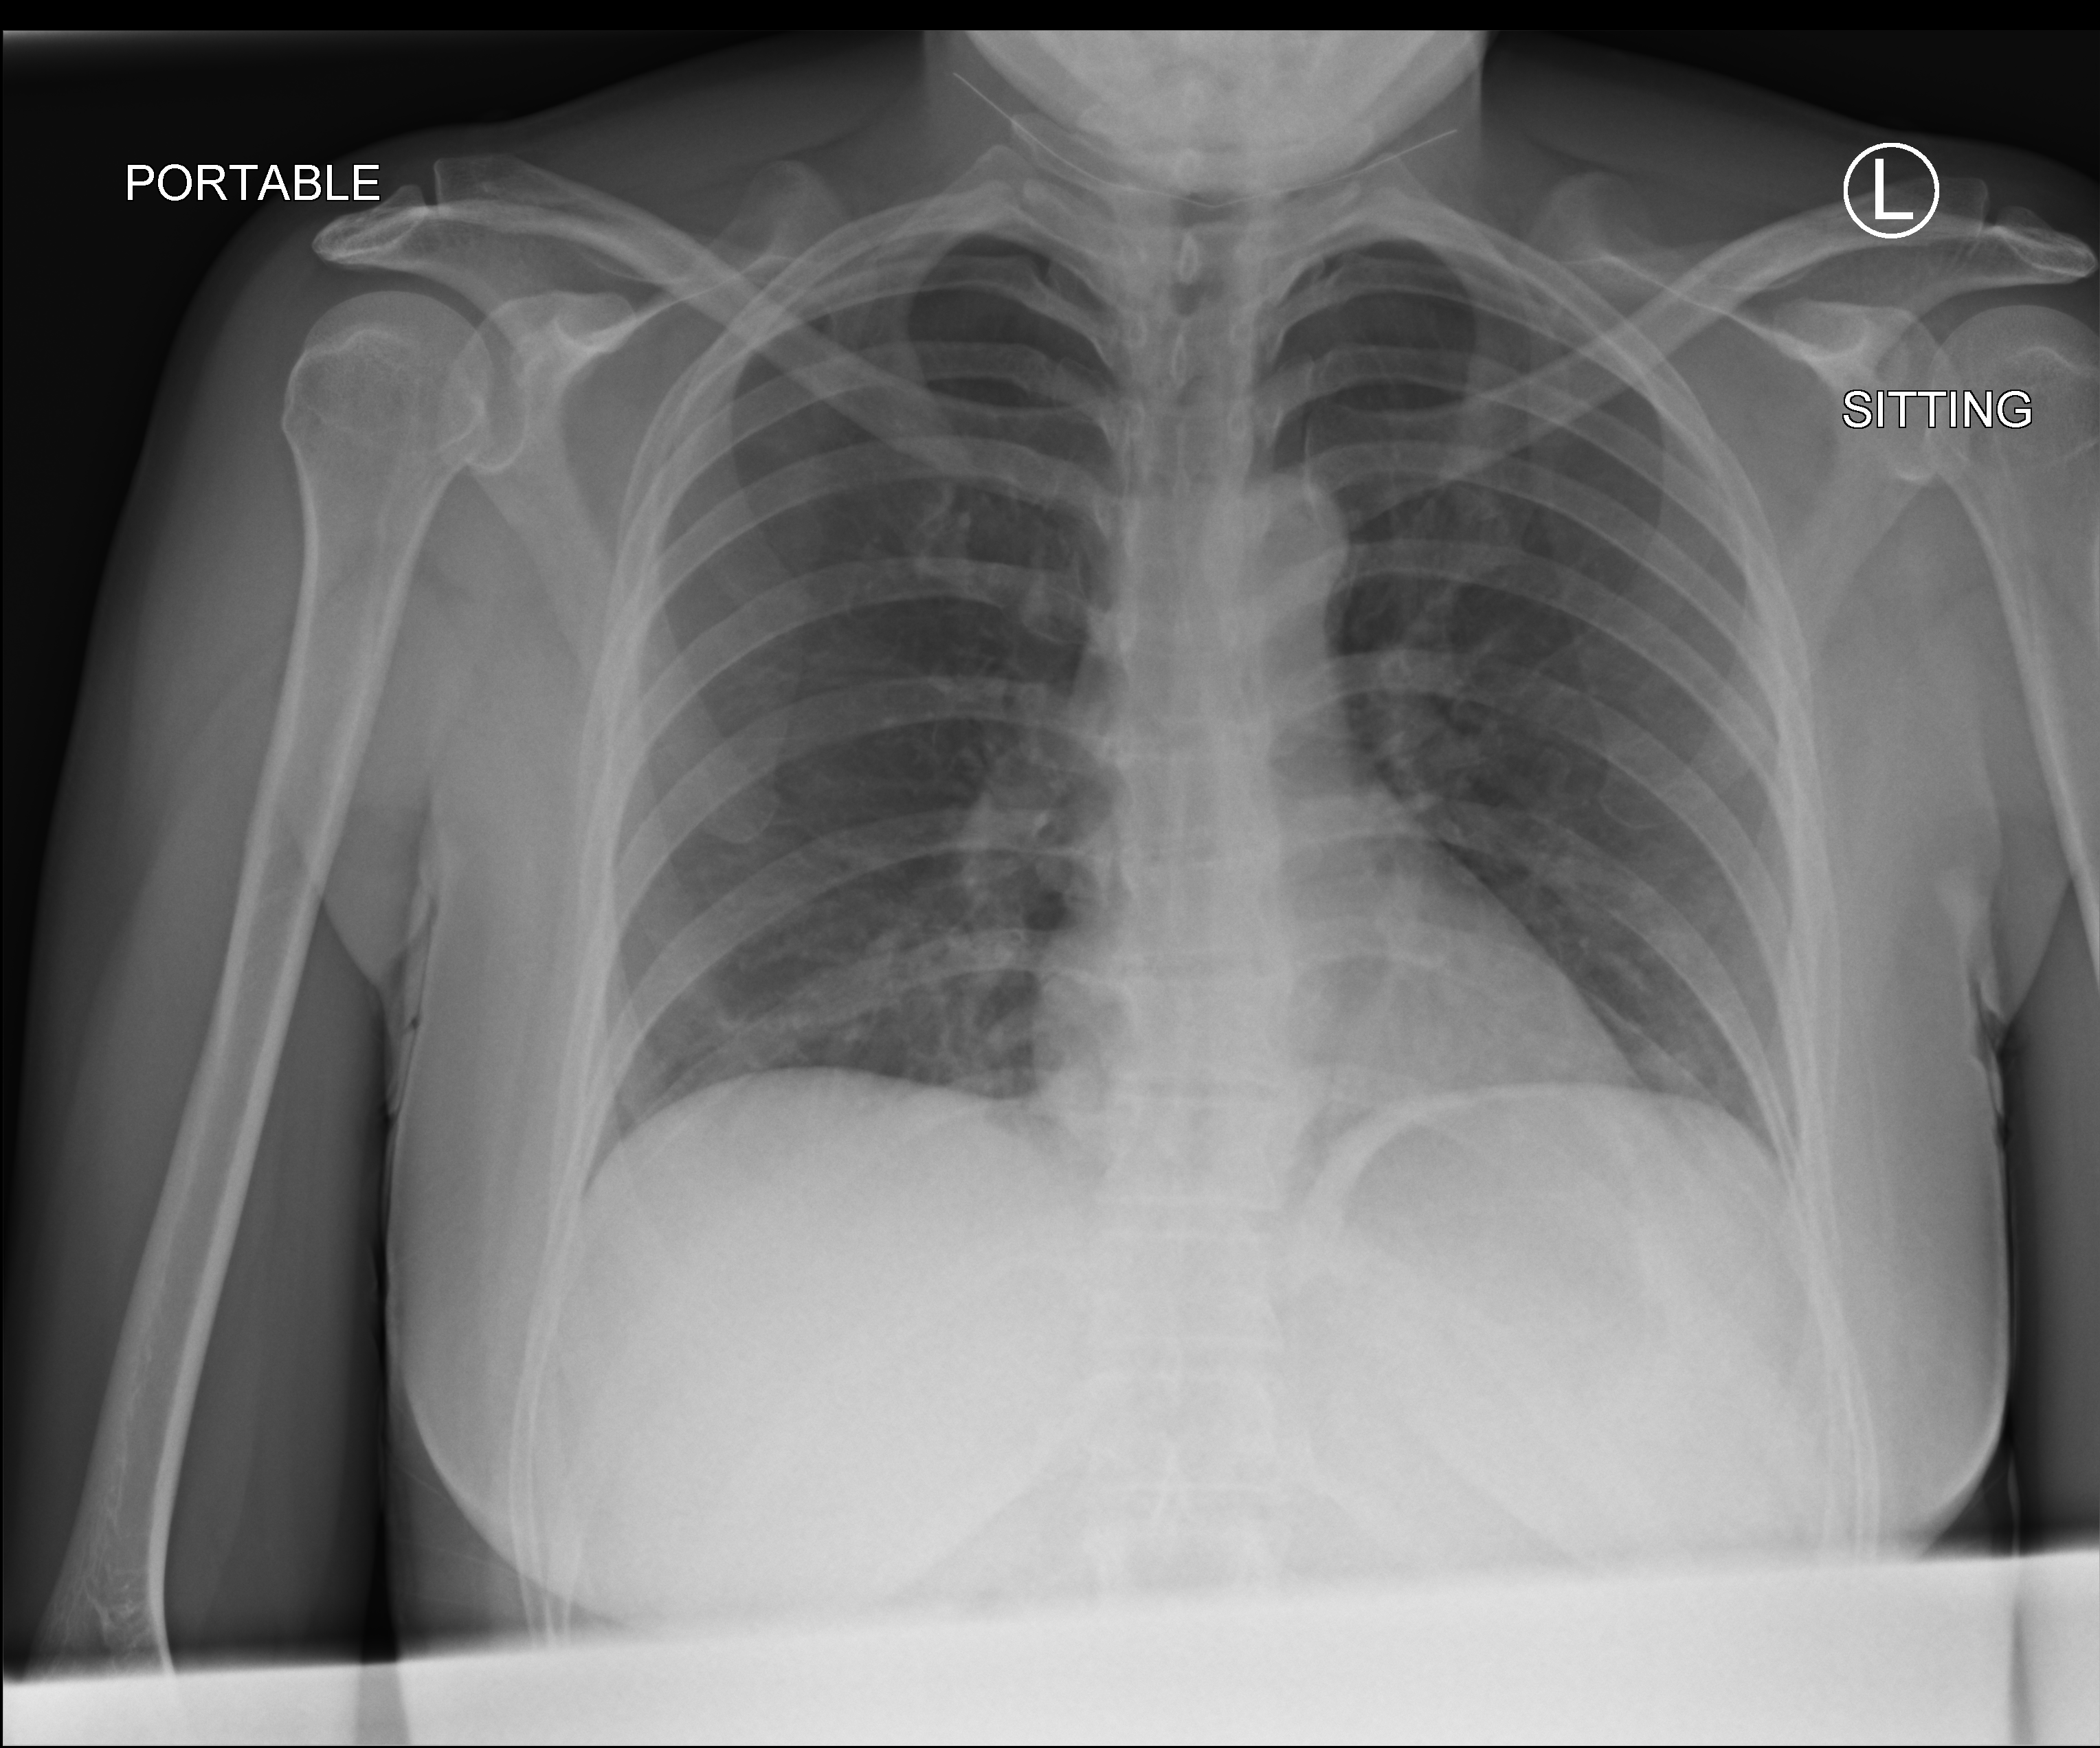
Chest X-ray (portable). Female patient hospitalised with COVID-19, age 18–59 years.
From the hospital-stay record, not from the radiograph (when in the stay this image was taken is not recorded): mechanically ventilated during this hospital stay: no; length of hospital stay: 1 day.